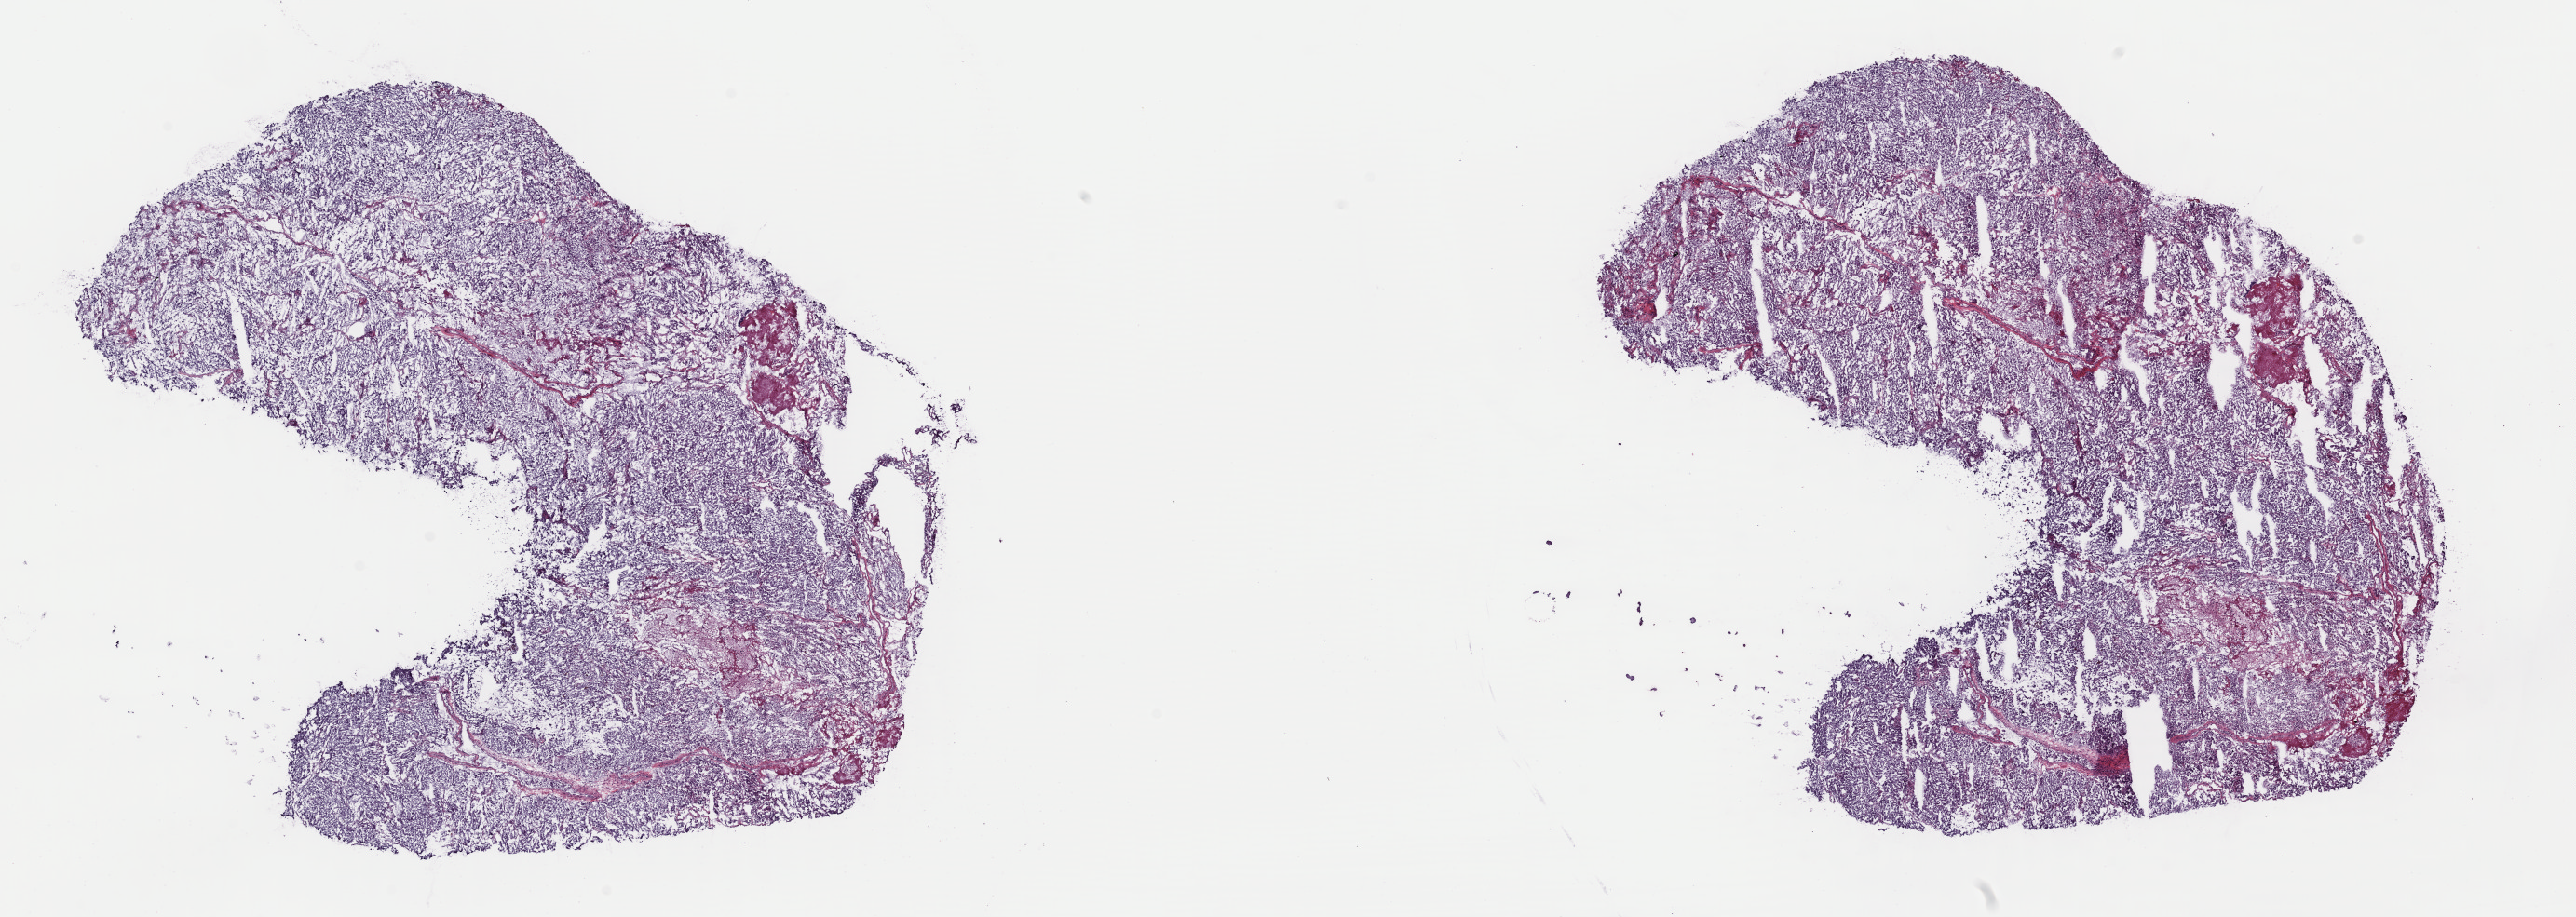
H&E-stained whole-slide image, low-resolution overview of the scanned area, about 21.8 x 7.8 mm. Frozen section from the top of the tissue portion. Primary tumour sample from the adrenal gland. Patient: male, age at initial diagnosis 43 years. Slide review estimates, as recorded: tumour cells 85%, tumour nuclei 100%, normal cells 0%, stromal cells 15%, necrosis 0%. Inflammatory infiltration, as recorded: lymphocyte infiltration 0%, monocyte infiltration 1%, neutrophil infiltration 0%.
• histologic diagnosis: Pheochromocytoma, malignant
• laterality: left